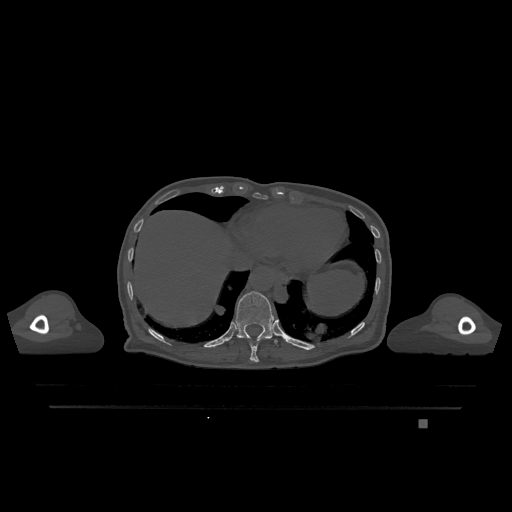
CT including the spine, one axial slice. Slice 608 of 1317 in the series (ordered by position). Bone window (W 1800 / L 400 HU). 0.5 mm slice thickness. 512 × 512 image matrix. Patient: female, 74 years. Case-level facts recorded for this patient, not image findings: primary cancer: lung; vertebrae with lytic lesions (as recorded): T1, T4, T5, T6, L4, L5.
Annotated regions visible in this slice (semi-automatic segmentation, software-assisted and operator-edited):
- T10 vertebra: bounding box (x1, y1, x2, y2) in pixels: (249, 342, 259, 362)
- T11 vertebra: (228, 291, 278, 344)